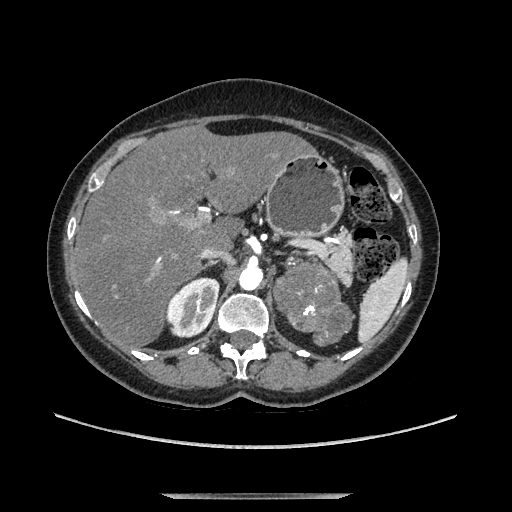
Contrast-enhanced abdominal CT, one axial slice. Position 82 of 169 along the scan axis. Soft-tissue window (W 400 / L 40 HU). 1.25 mm slice thickness. 512 × 512 image matrix, field of view 400 × 400 mm. Female patient. Case-level facts recorded for this patient, not image findings: diagnosis: adrenocortical carcinoma; tumour side: left adrenal; tumour size at pathology: 9 cm; Ki-67 index: 2 %; stage (as recorded): 3.
Annotated regions visible in this slice (semi-automatically segmented with operator editing):
- mass: bounding box (x1, y1, x2, y2) in pixels: (277, 268, 349, 342)